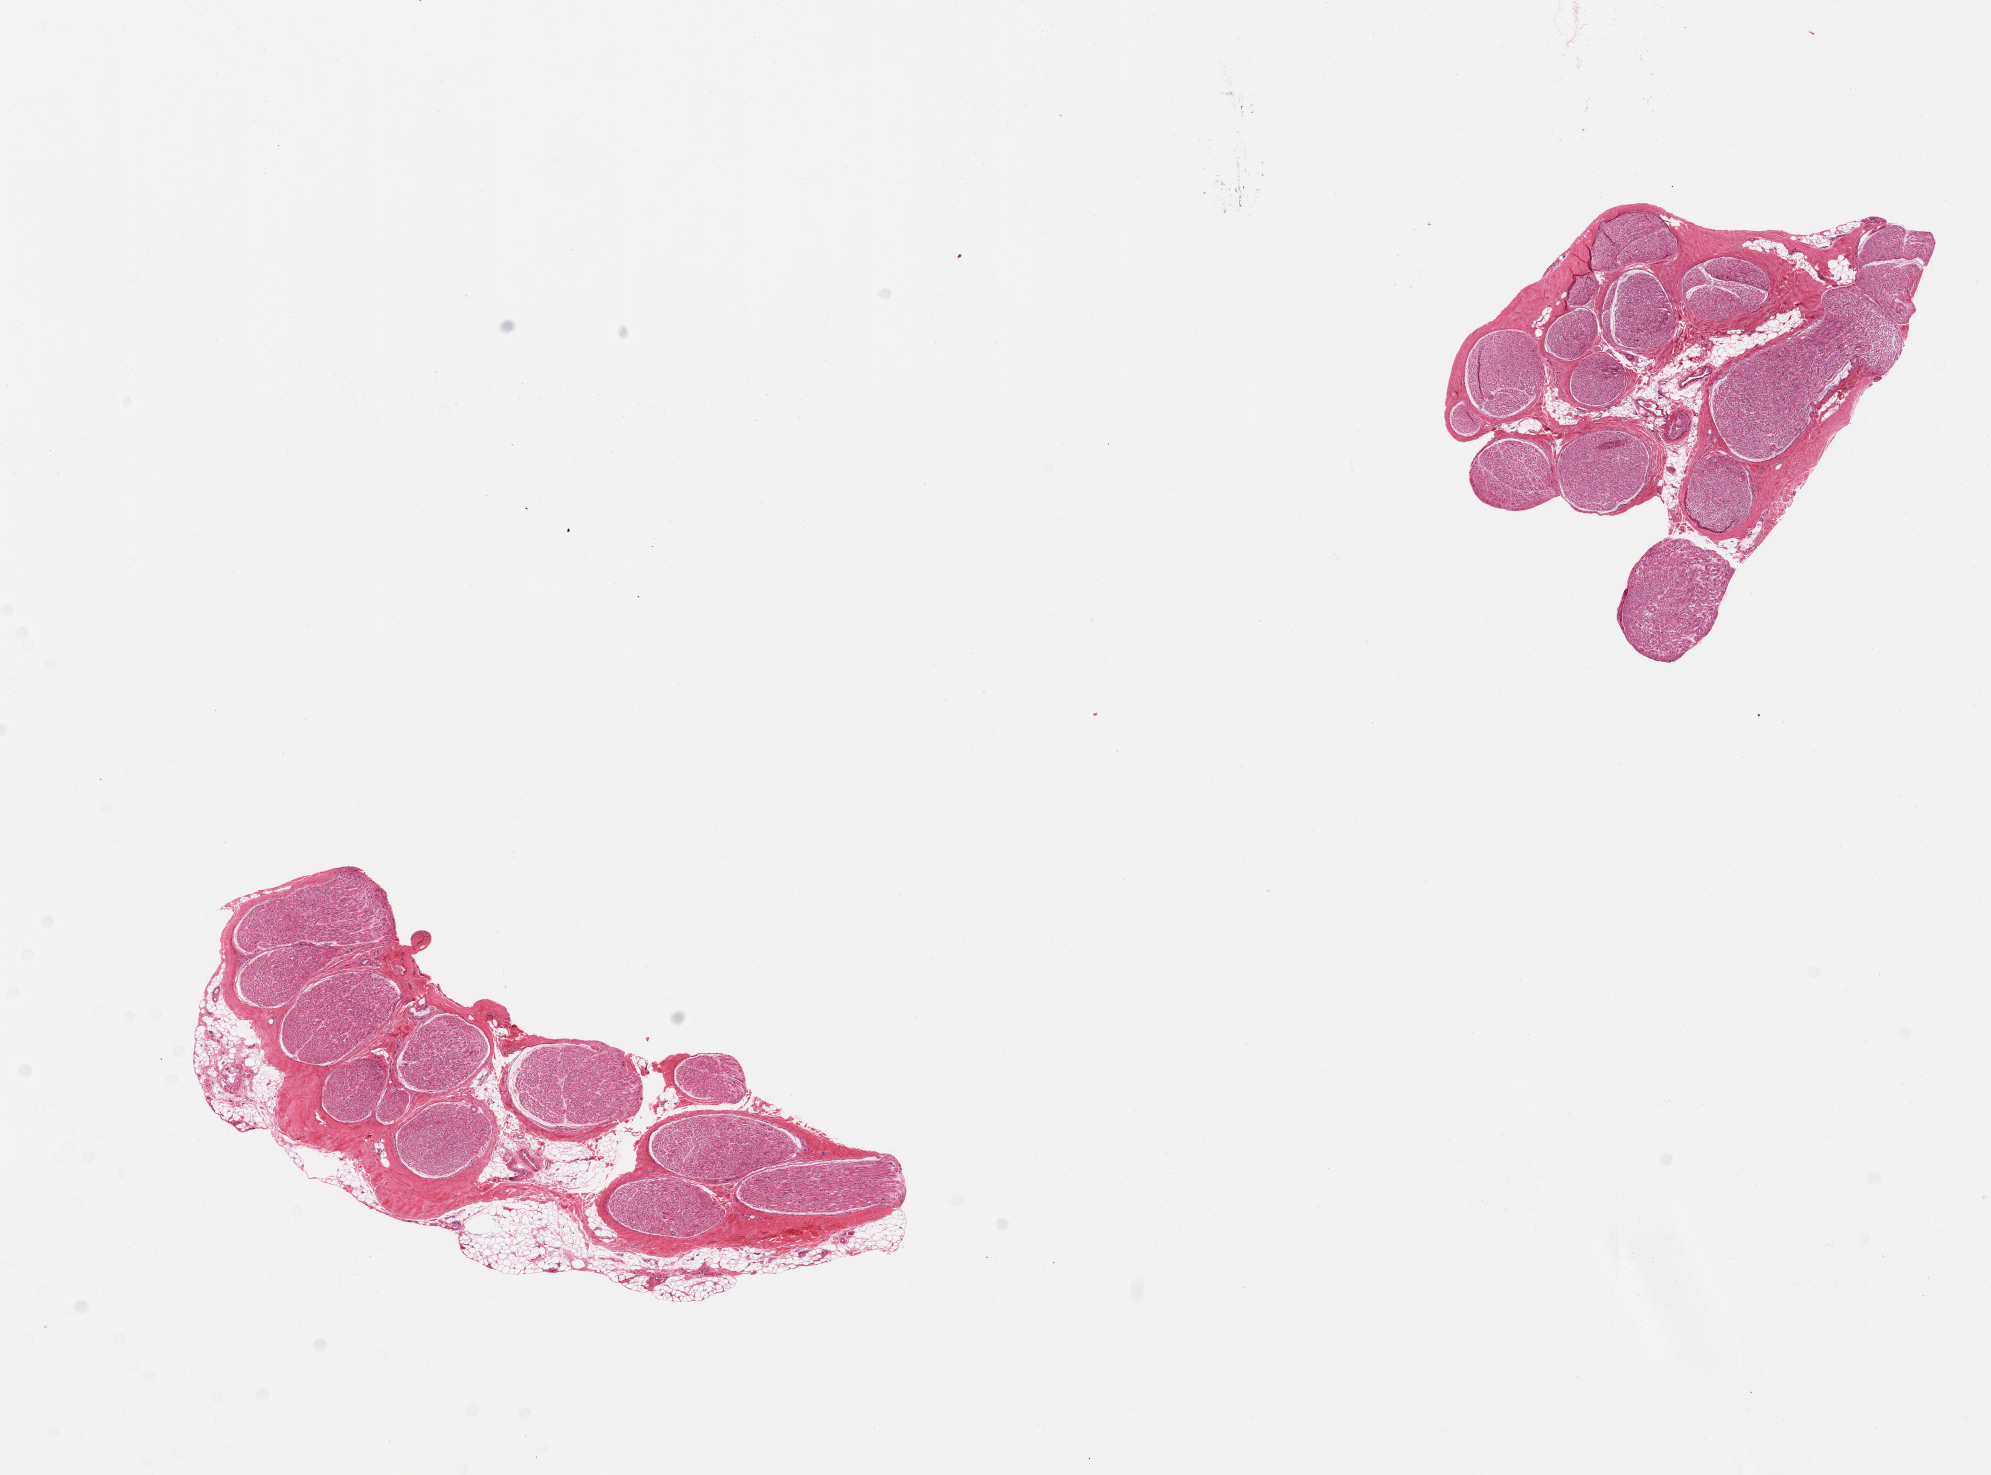
H&E whole-slide image — whole scanned area (about 15.8 x 11.7 mm) shown as a low-resolution overview. PAXgene-fixed, paraffin-embedded tissue. Target tissue: tibial nerve. Donor tissue sample.
Review note (as recorded): 2 pieces, good specimens, one section with ~0.5mm rim of fat along one edge.